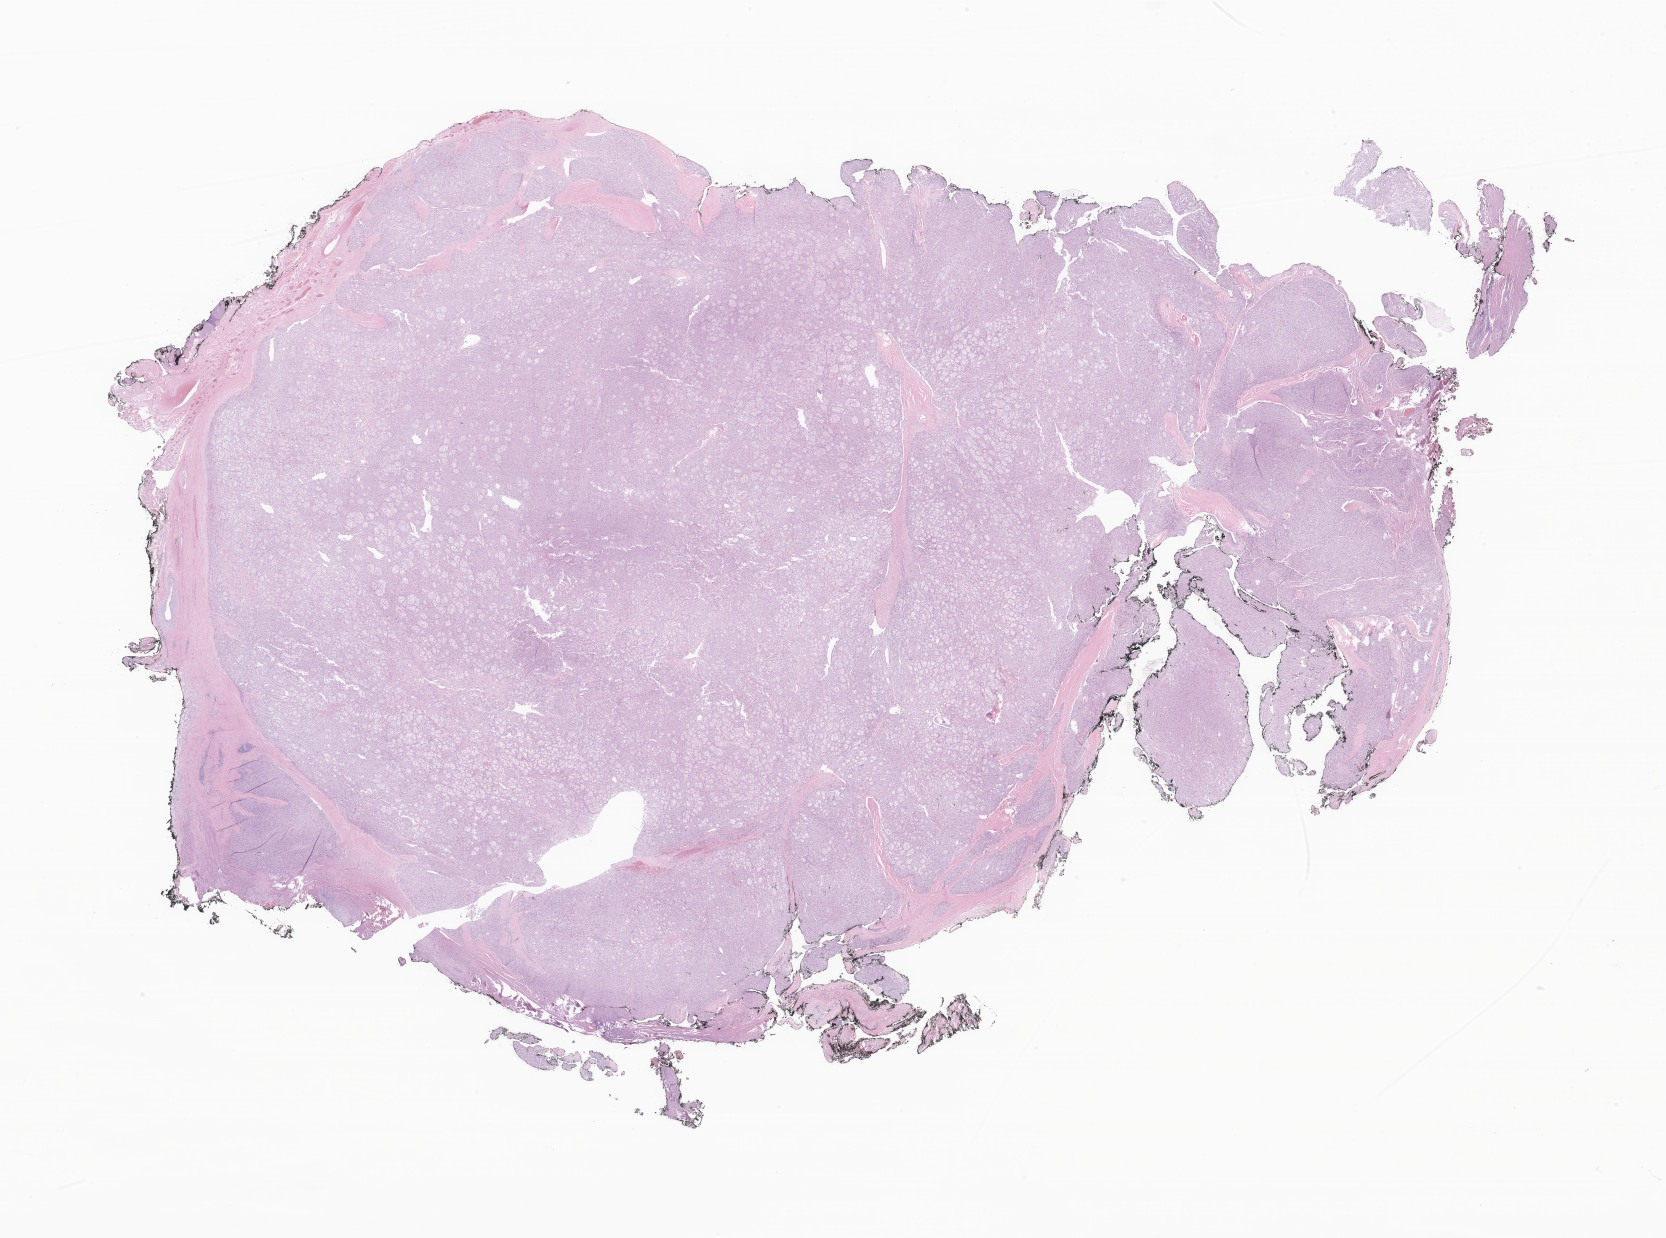
Whole-slide image, hematoxylin and eosin (H&E) stain of tumor tissue from the parotid gland, low-resolution overview of the scanned area, about 28.1 x 20.9 mm; formalin-fixed, paraffin-embedded (FFPE) tissue. Male patient, age 97 months (8 years 1 month).
Diagnosis (ICD-O-3 morphology term): Acinar cell carcinoma.